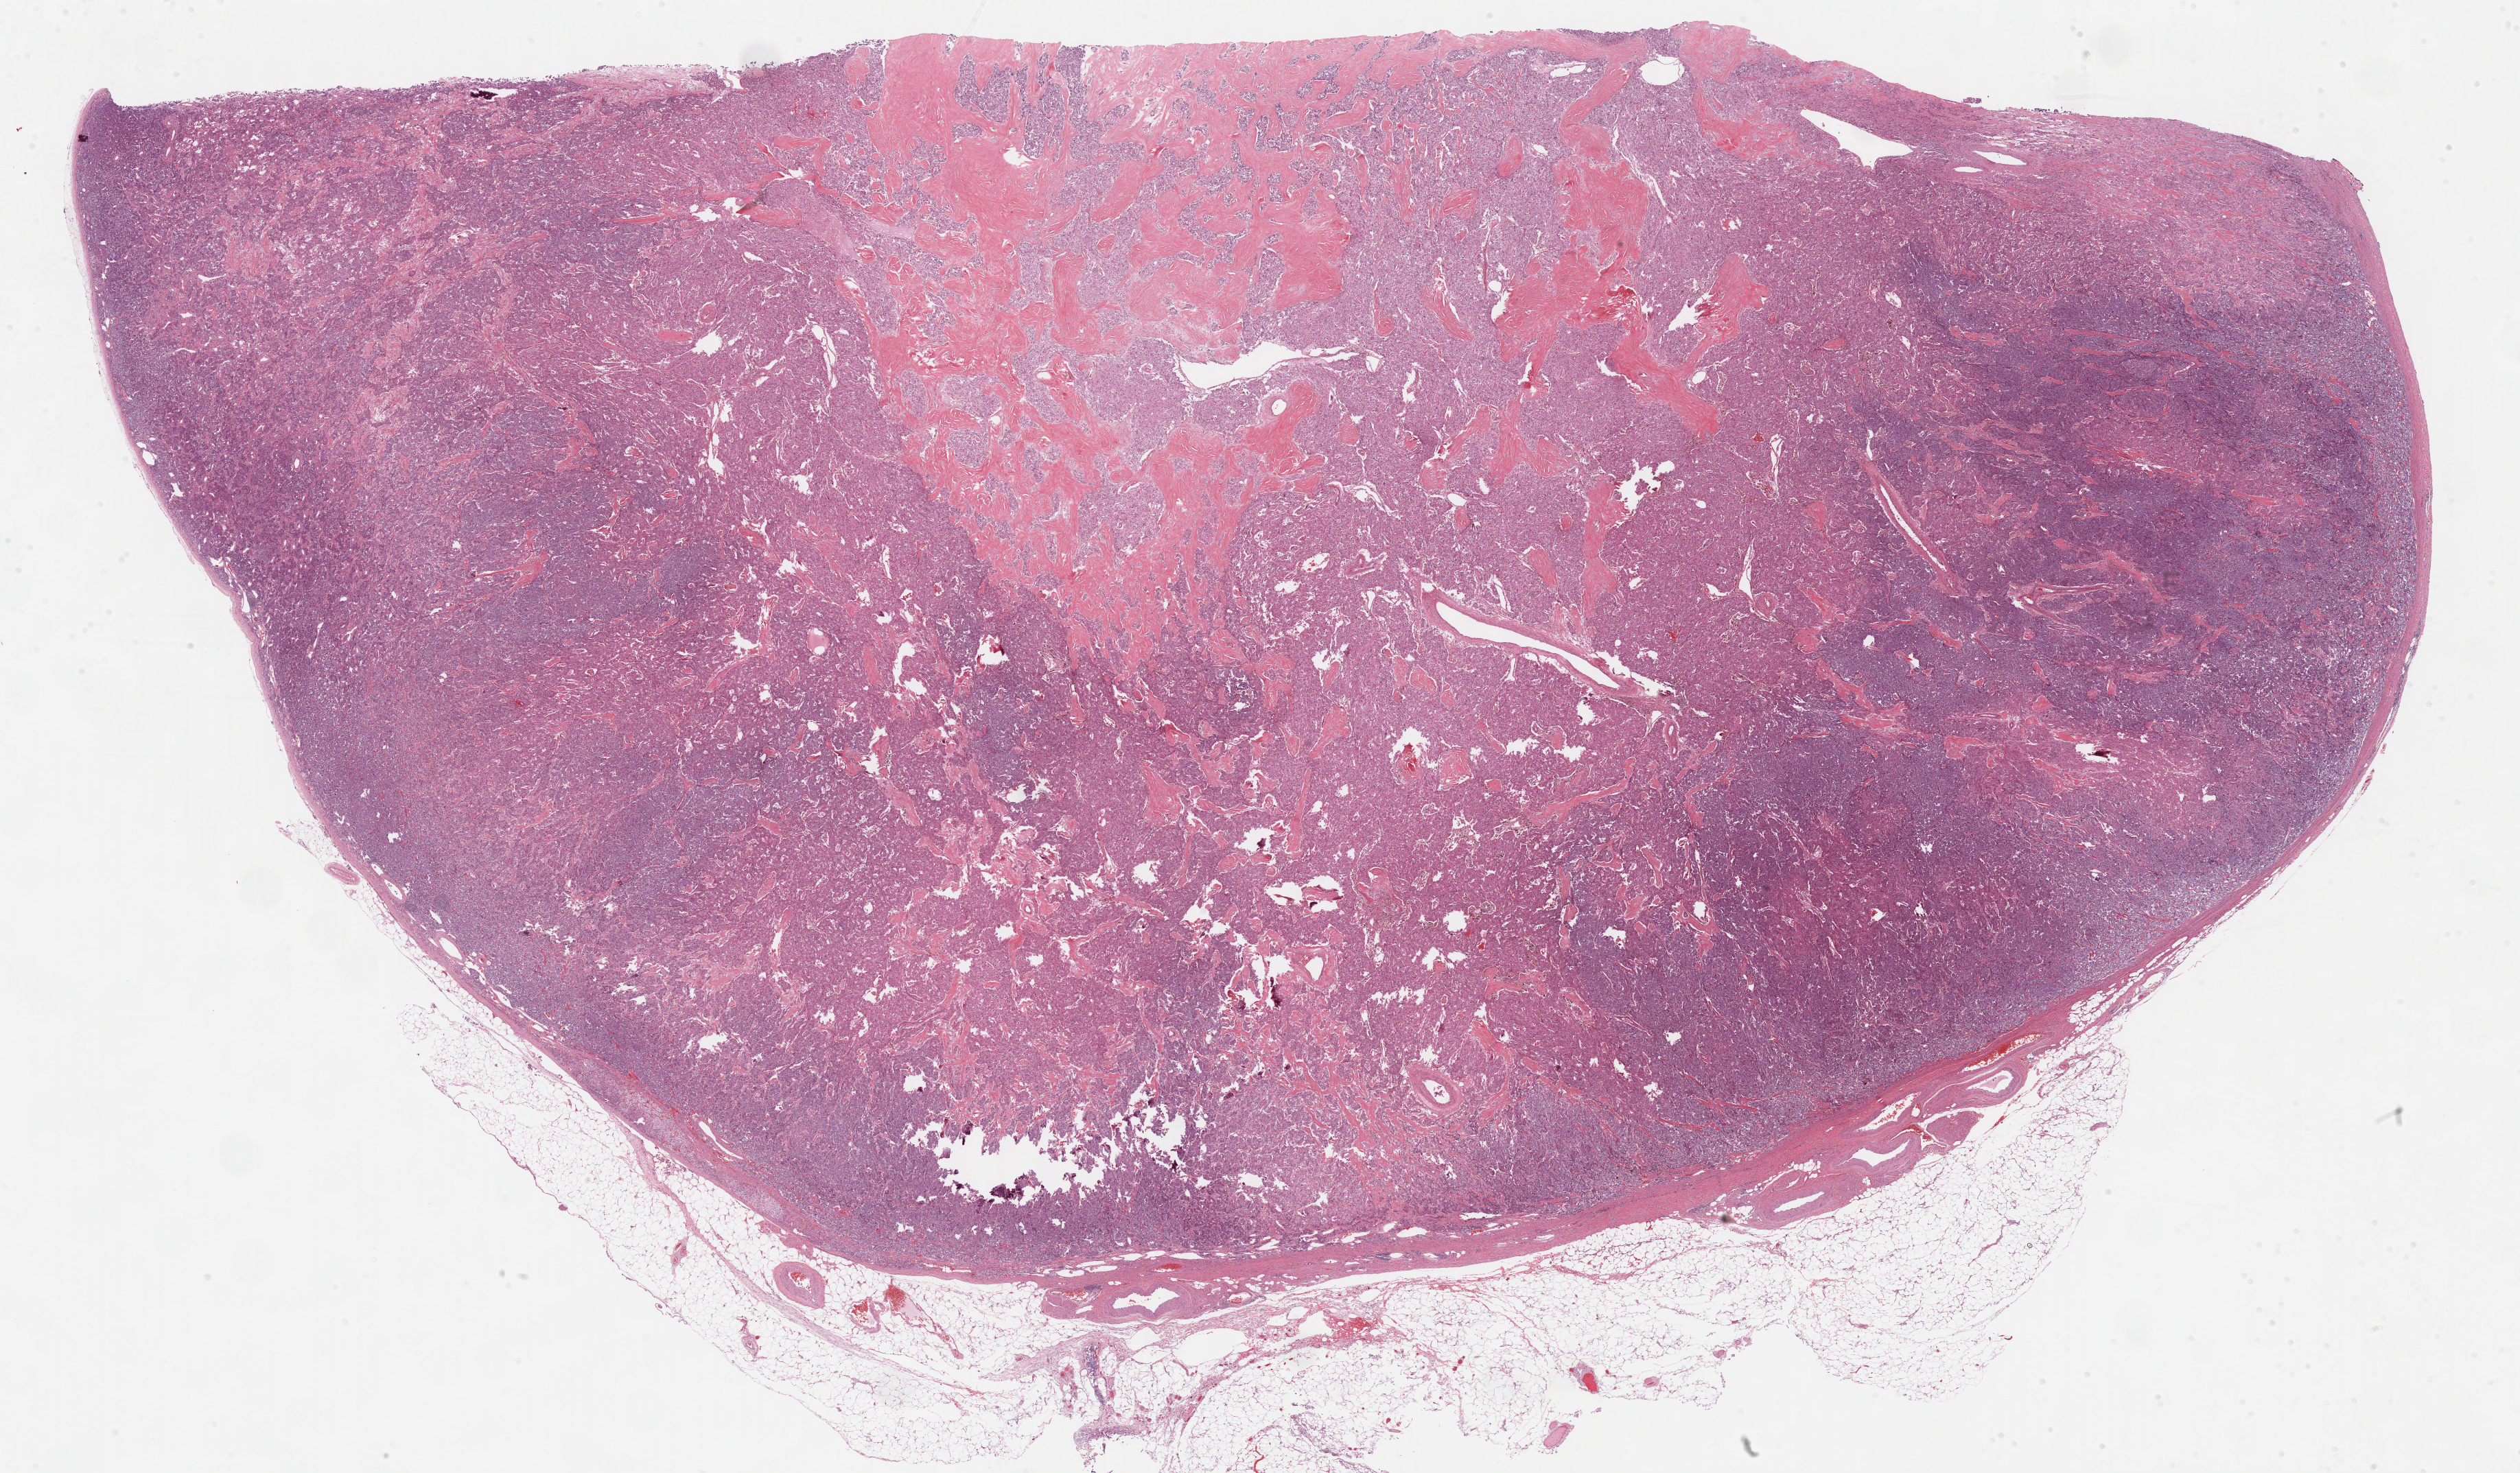
Digitized Hematoxylin and eosin (H&E) stained tissue section (whole slide) — whole scanned area (about 29.7 x 17.4 mm) shown as a low-resolution overview, formalin-fixed paraffin-embedded (FFPE) diagnostic section, primary tumour sample from the adrenal gland. Female patient; age at initial diagnosis 70 years.
Laterality: right. Histologic diagnosis: Pheochromocytoma, NOS.